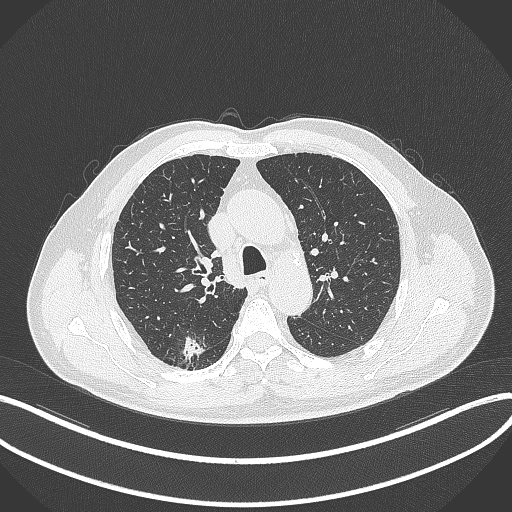
Chest CT, one axial slice. Reconstruction kernel B70f. 120 kVp. Lung window (W 1500 / L -600 HU). 1 mm slice thickness. 512 × 512 image matrix, field of view 400 × 400 mm. Patient: male, 69 years. From the clinical record (not read from this slice): clinical TNM (as recorded): T1b N0 M0.
Outlined on this slice (rectangle marked by the reading radiologist):
- lung tumour (recorded histology: adenocarcinoma): bounding box (x1, y1, x2, y2) in pixels: (176, 333, 207, 364)